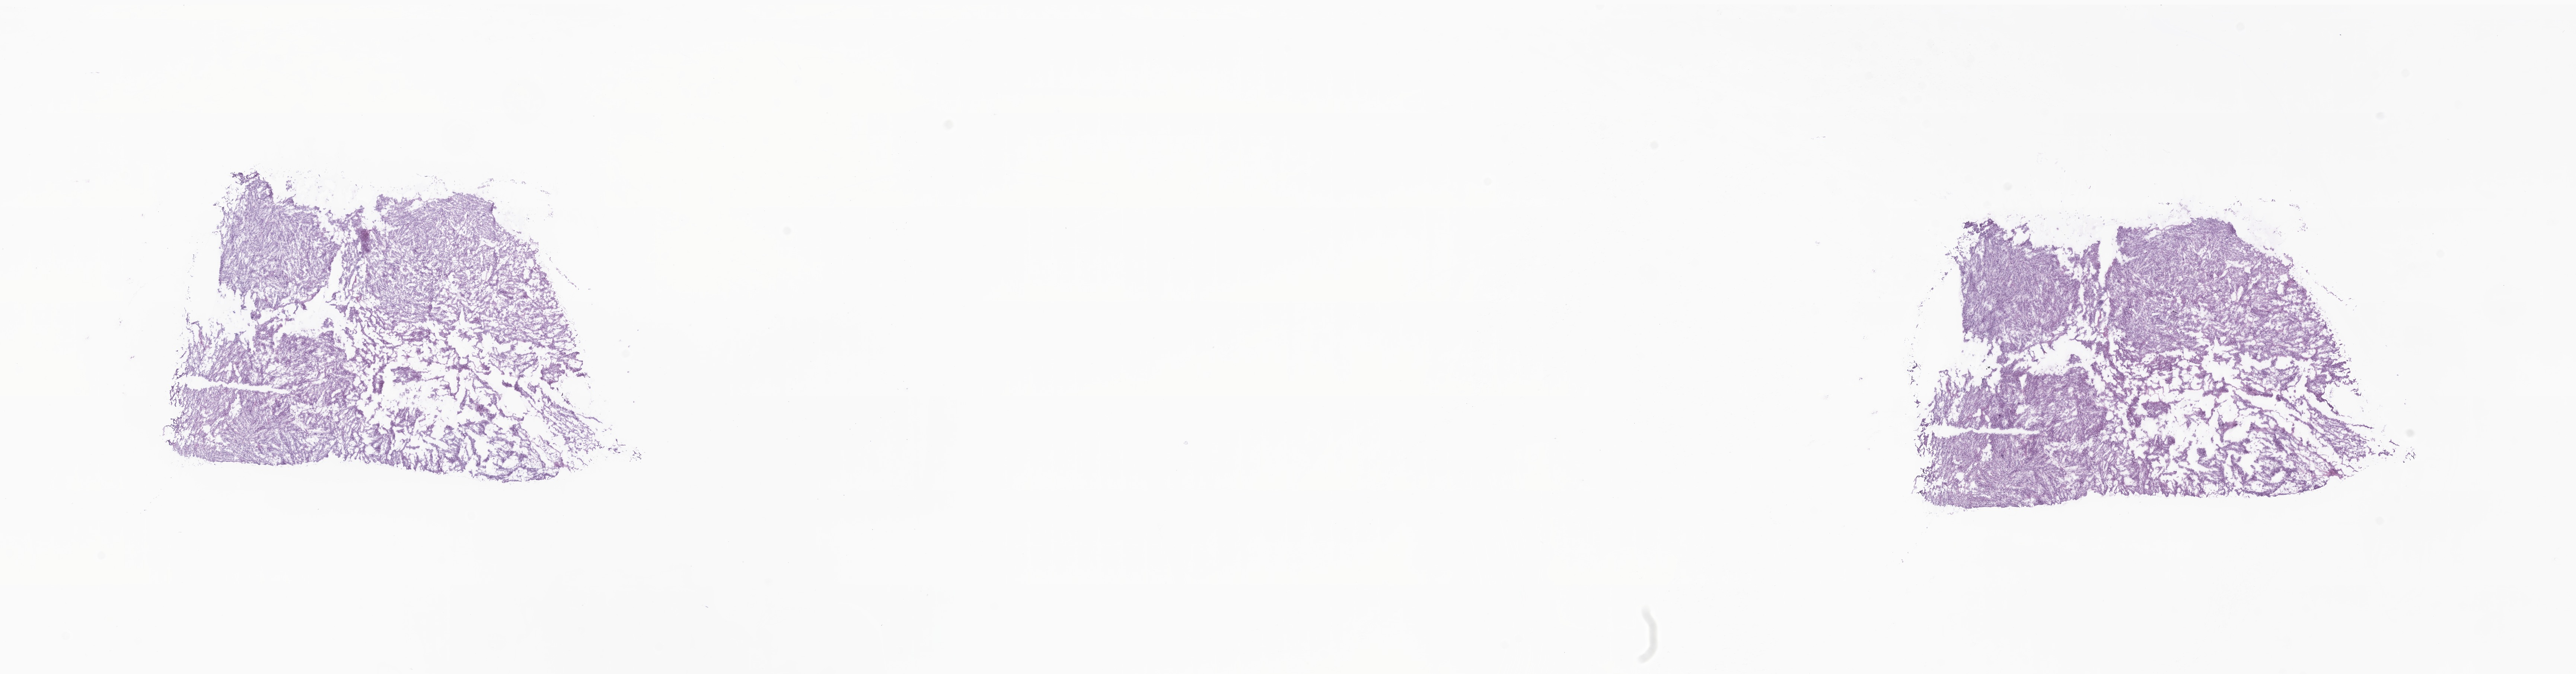
Digitized haematoxylin and eosin-stained section — low-resolution overview of the scanned area, about 29.2 x 7.6 mm, frozen section (tissue freezing medium), specimen: metastatic tumor tissue, resected from abdomen. Patient: female, age at initial diagnosis 48 years. Slide review estimates, as recorded: tumor cells 90%, tumor nuclei 90%, stromal cells 10%, necrosis 0%, normal cells 0%. Infiltration values recorded for this section: lymphocyte infiltration 0%, monocyte infiltration 0%, neutrophil infiltration 0%.
* patient diagnosis (primary): Leiomyosarcoma, NOS